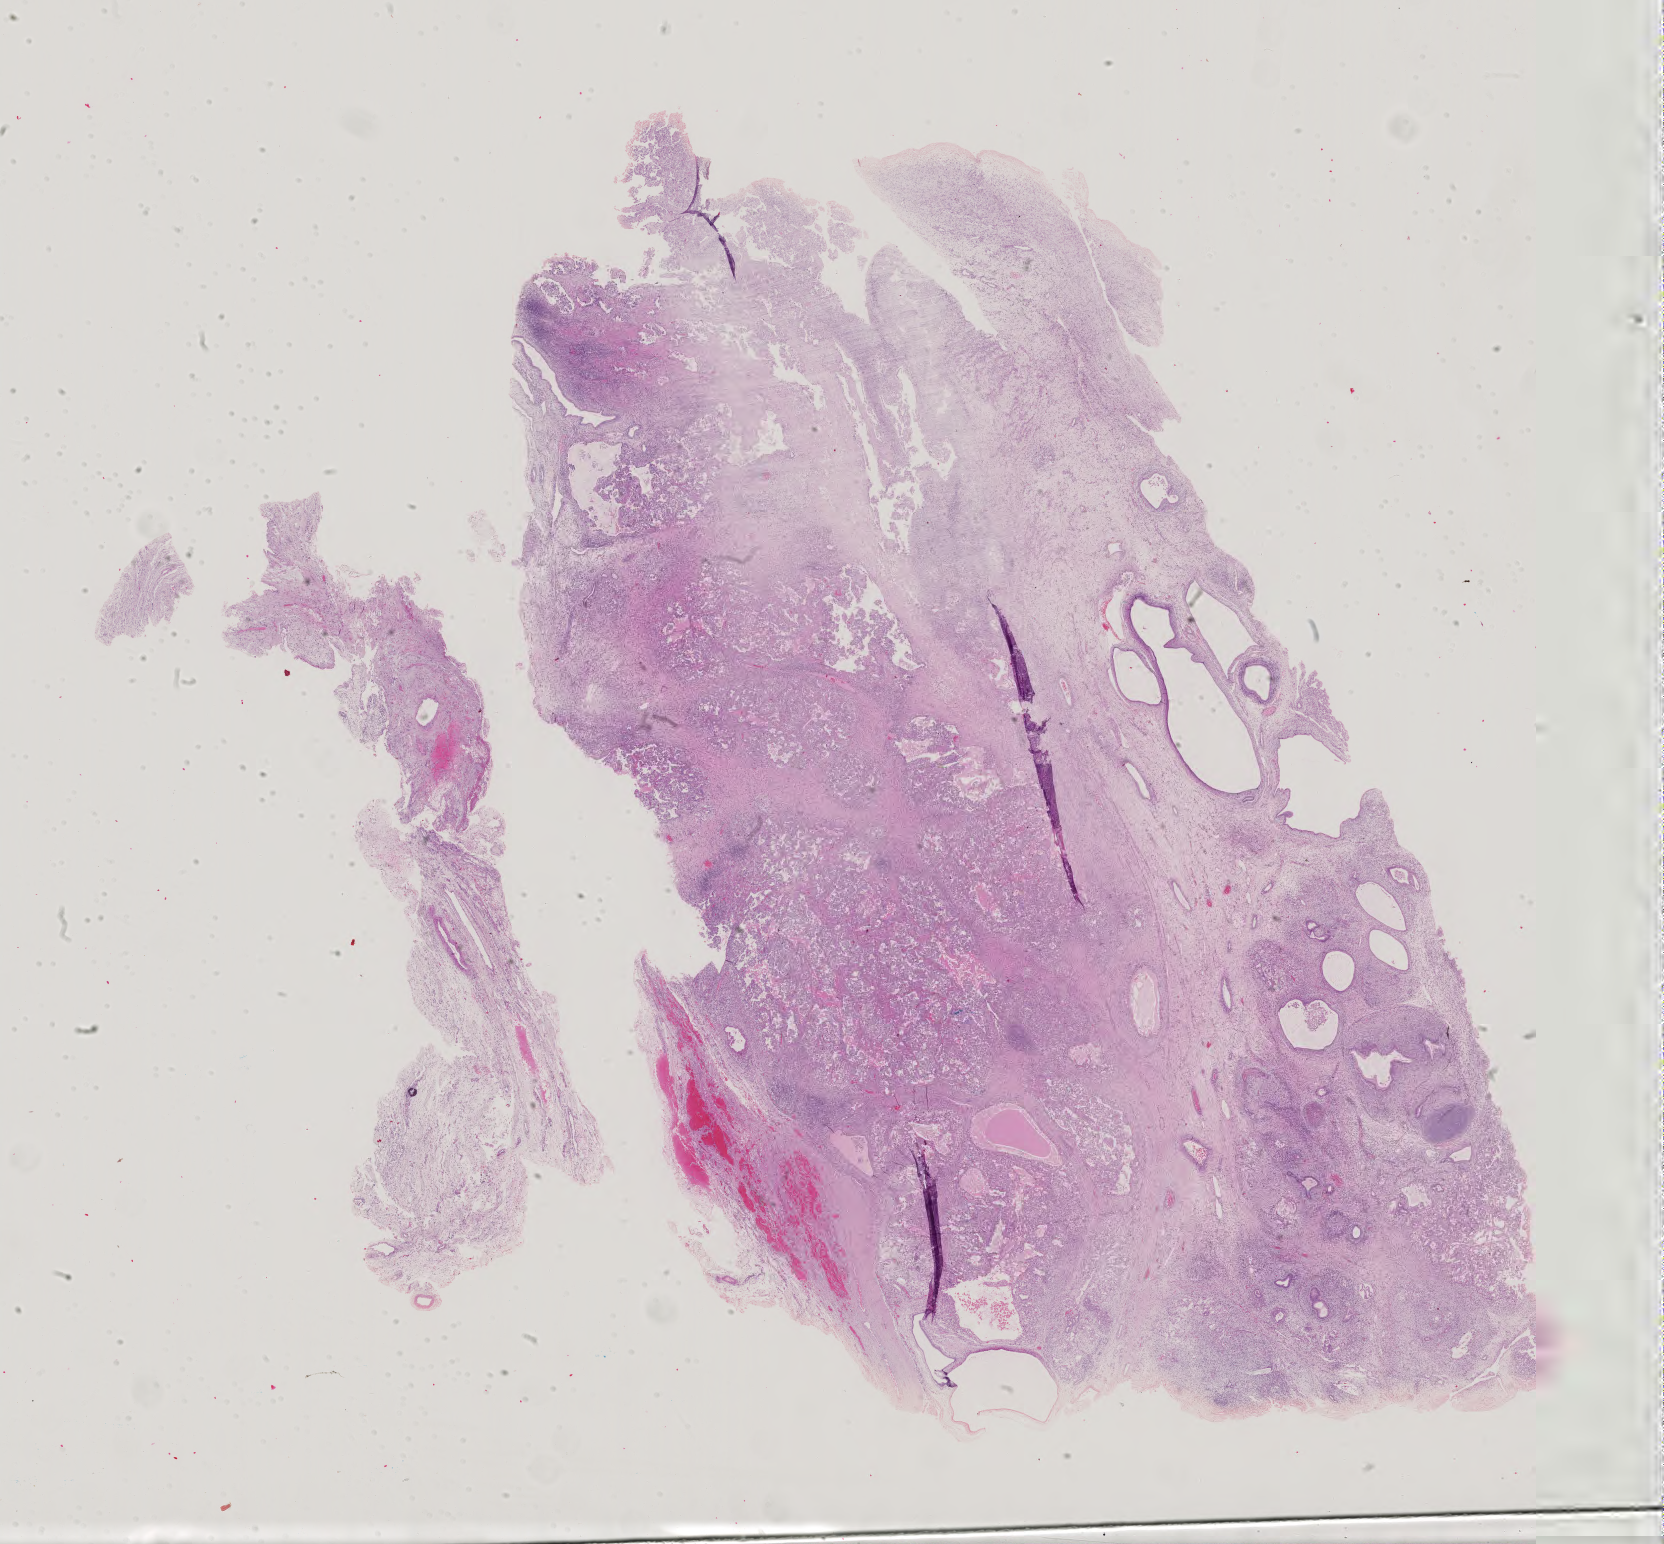
Hematoxylin and eosin (H&E) stained whole-slide image, shown as a low-resolution overview of the whole scanned area (about 24.2 x 22.5 mm). Patient sex: male.
Specimen: formalin-fixed paraffin-embedded (FFPE) diagnostic section; primary tumour sample from the testis.